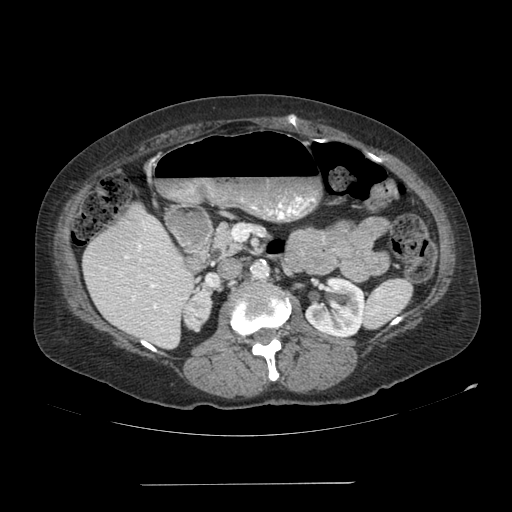
Contrast-enhanced abdominal CT, one axial slice; slice 49 of 113 in the series (ordered by position); reconstruction kernel SOFT; soft-tissue window (W 400 / L 40 HU); 2.5 mm slice thickness; 512 × 512 image matrix, field of view 440 × 440 mm. Female patient, age 67 years. Case-level facts recorded for this patient, not image findings: diagnosis: adrenocortical carcinoma; tumour side: right adrenal; tumour size at pathology: 9.8 cm; Ki-67 index: 59 %; stage (as recorded): 4.
Structures marked on this image (semi-automatically segmented with operator editing):
- mass: bounding box [x1, y1, x2, y2] px = [184, 291, 210, 329]